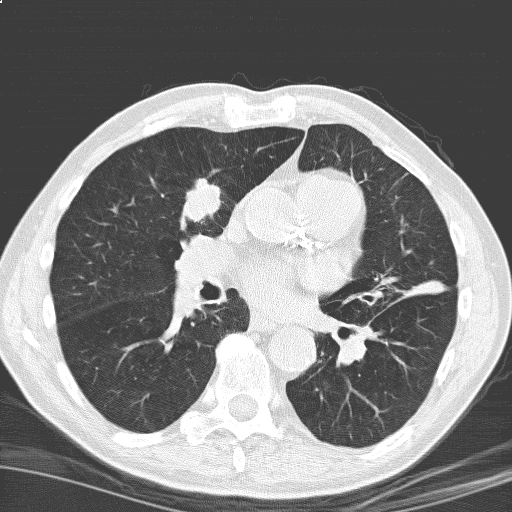
Low-dose screening chest CT, one axial slice; position 95 of 184 along the scan axis; 120 kVp; lung window (W 1500 / L -600 HU); 3.2 mm slice thickness; 512 × 512 image matrix, field of view 329 × 329 mm.
Annotated regions visible in this slice (manually delineated by an expert):
- lesion 1 (tumor, upper lobe of right lung): bounding box (x1, y1, x2, y2) in pixels: (182, 179, 220, 222)